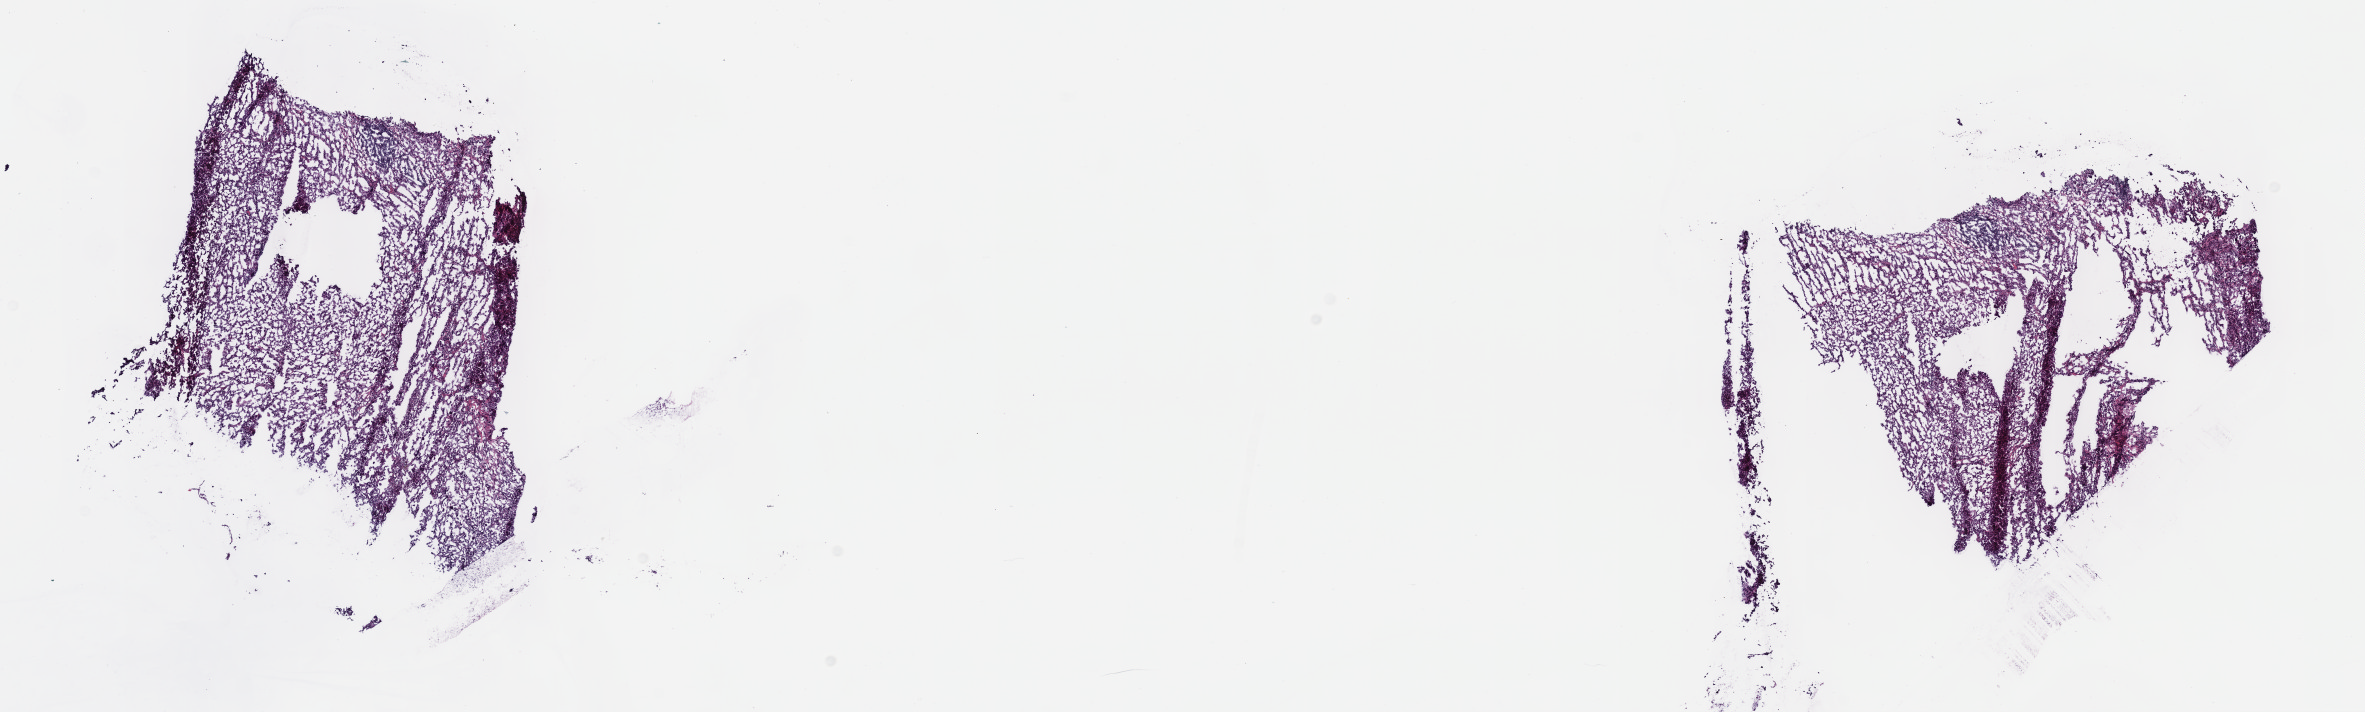
H&E whole-slide image, whole scanned area (about 19.1 x 5.8 mm, from a 40x scan) shown as a low-resolution overview. Frozen section from the top of the tissue portion. Metastatic tumour sample. Male patient; age at initial diagnosis 48 years. Composition of this section per pathologist review: tumour cells 90%, tumour nuclei 95%, normal cells 0%, stromal cells 10%, necrosis 0%. Infiltration values recorded for this section: lymphocyte infiltration 0%, monocyte infiltration 0%, neutrophil infiltration 0%.
- this section: metastatic tumour tissue
- patient diagnosis: Malignant melanoma, NOS